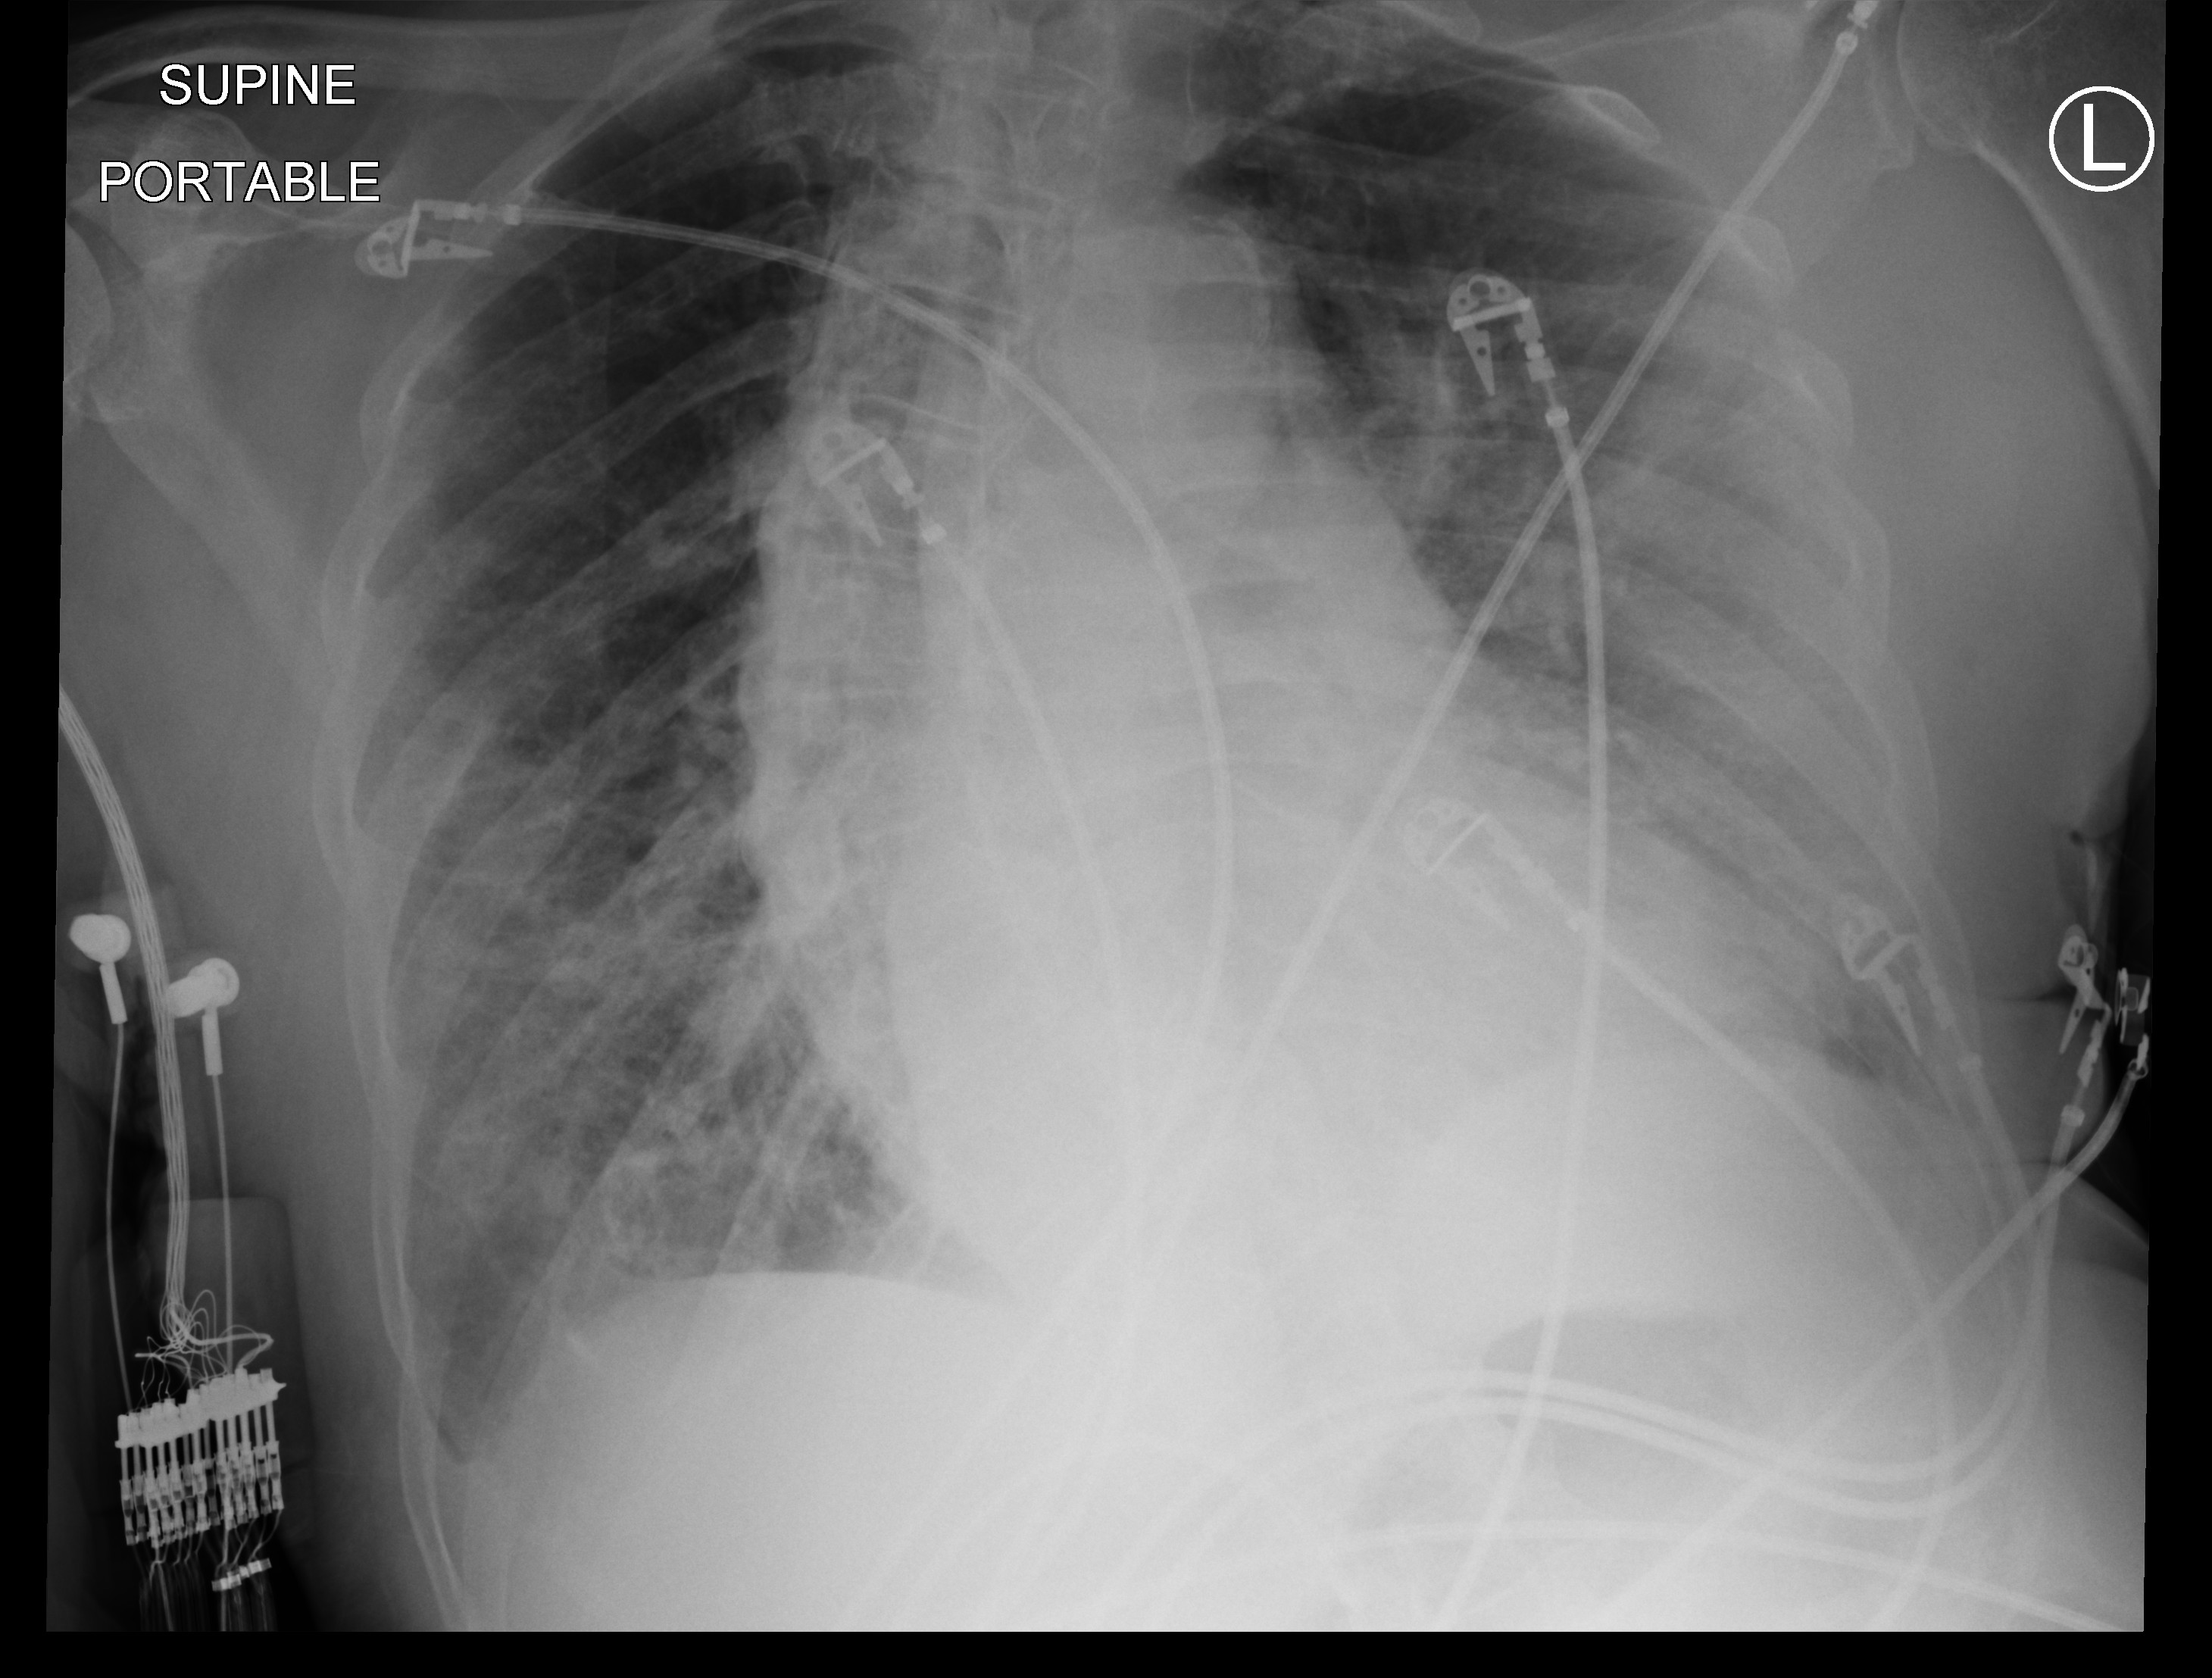
Chest X-ray (portable); anteroposterior (AP) projection. Patient hospitalised with COVID-19; male, aged 75–90 years.
Hospital-stay facts (about this admission, not read from this image; timing relative to this image not recorded):
- admitted to intensive care during this hospital stay: no
- mechanically ventilated during this hospital stay: no